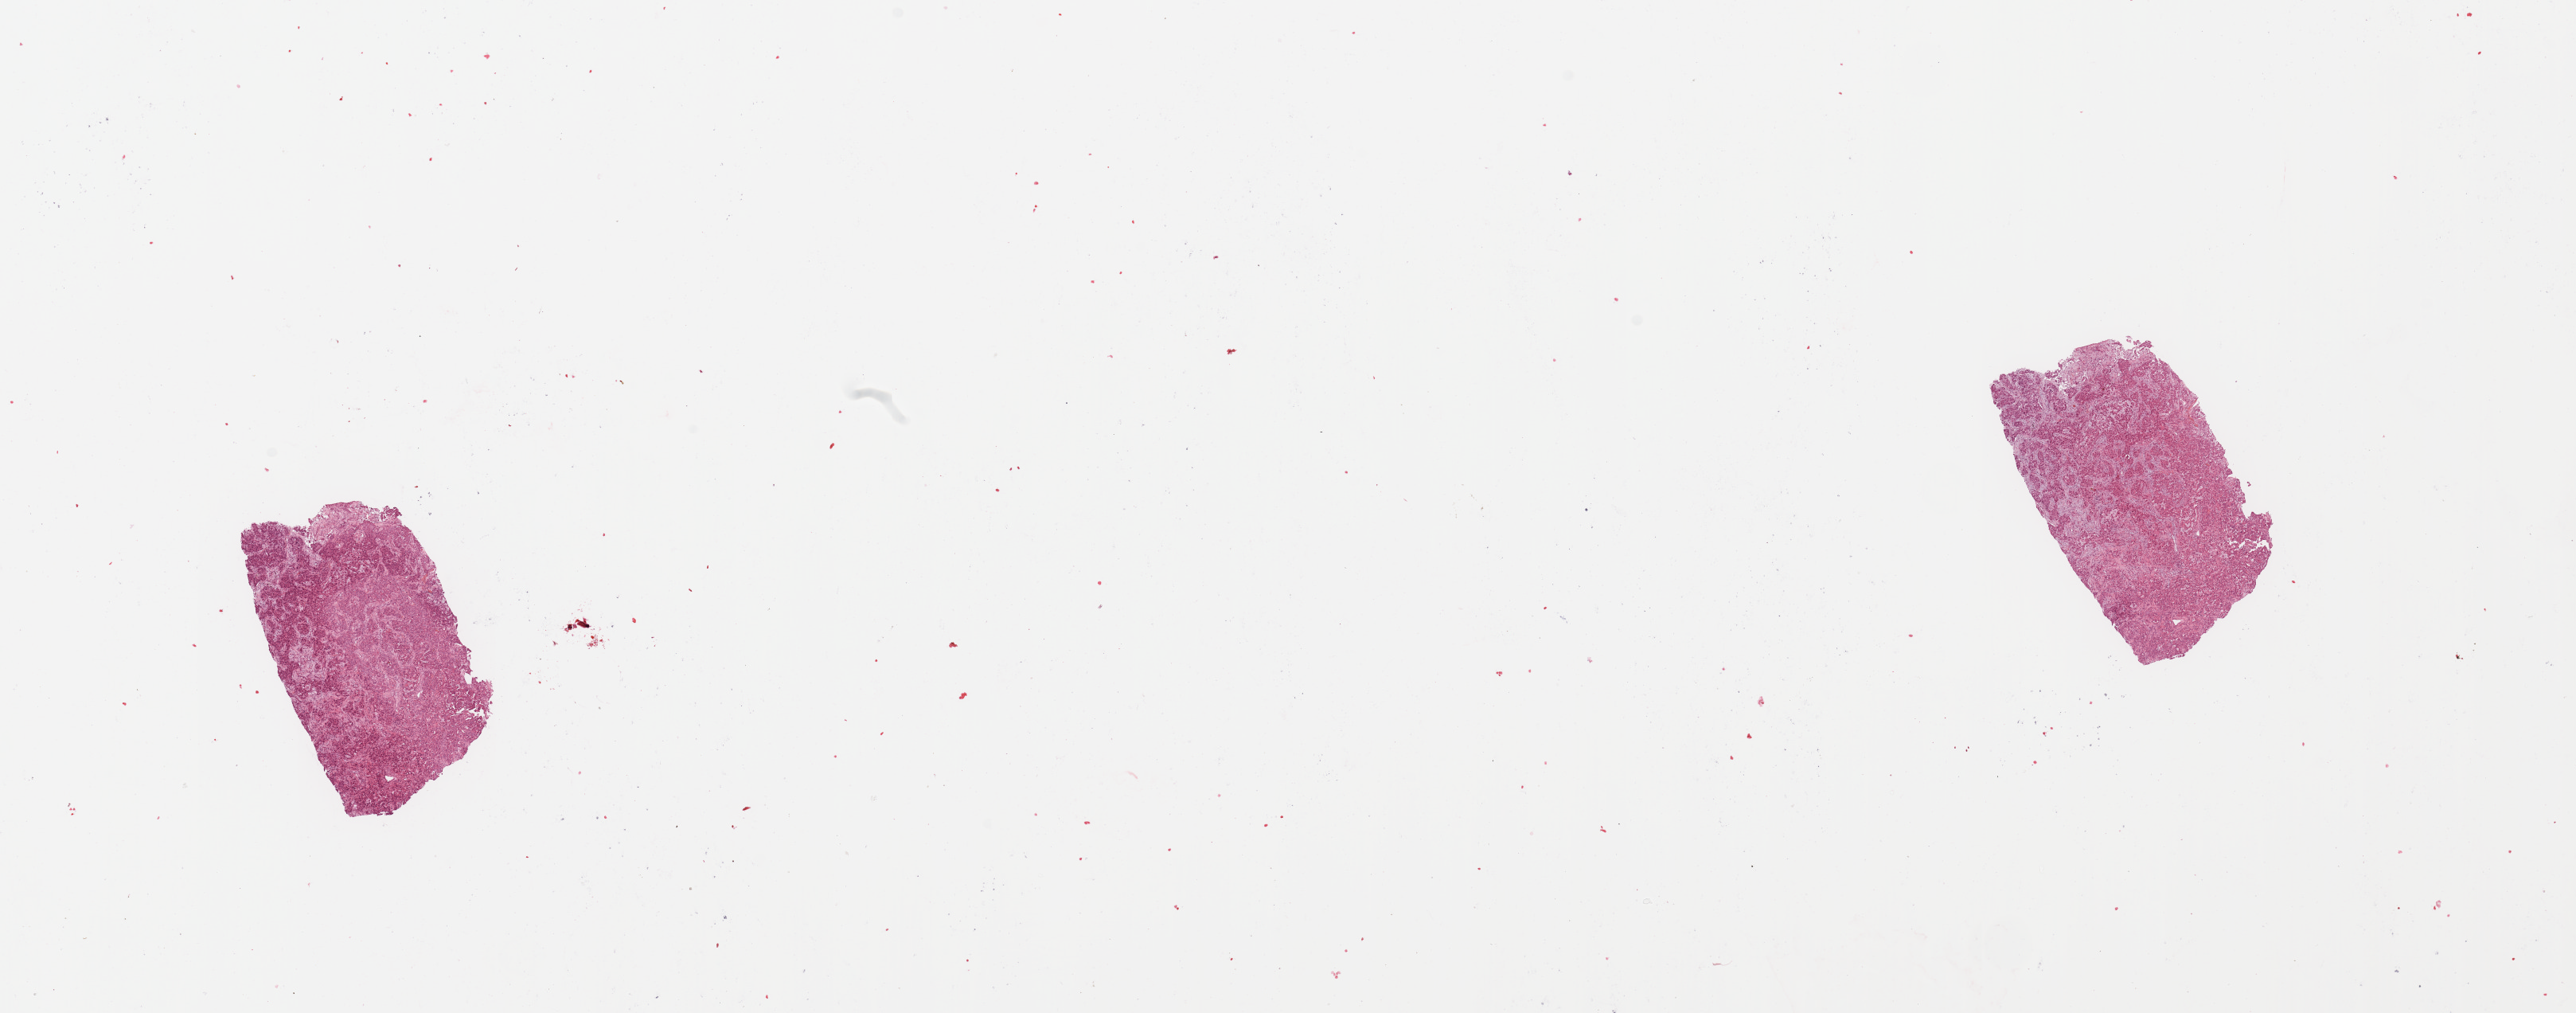
Whole-slide histology image, Hematoxylin and eosin (H&E) stained — shown as a low-resolution overview of the whole scanned area (about 25.6 x 10.1 mm); tumour tissue sample, sampled site: lung. Male, 51 y/o. Histologic grade: G2 (moderately differentiated). Pathologist review of this section (percent, as recorded): tumour nuclei 85%, necrosis 0%.
- diagnosis: Adenocarcinoma, NOS
- primary tumour site (as recorded): left upper lobe
- AJCC pathologic stage: IB